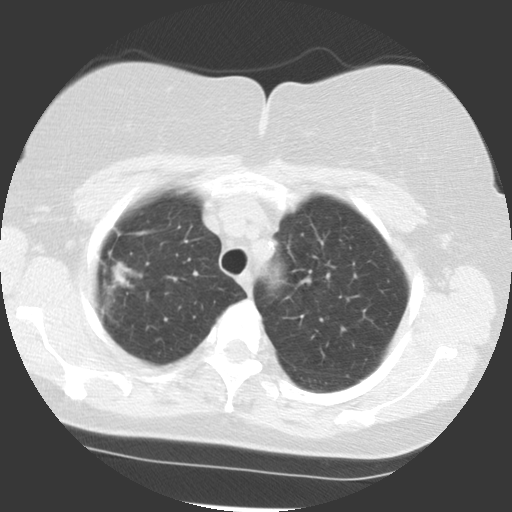
Axial slice from a low-dose chest CT screening exam, first (baseline) screen, lung window (W 1500 / L -600 HU), 2.5 mm slice thickness, standard (soft-tissue) reconstruction kernel (STANDARD), 140 kVp, slice 93 of 113 in the series, 512 × 512 image matrix. Female participant, aged 68 years at enrolment. Former smoker at enrolment.
• Expert reader's lesion annotation, box from (x=91, y=253) to (x=145, y=311) px.
• The exam's reader record, not a measurement of the box and not confirmed to be the same lesion: non-calcified nodule or mass ≥4 mm, right upper lobe, 42 × 20 mm, spiculated (stellate) margins, soft tissue attenuation.